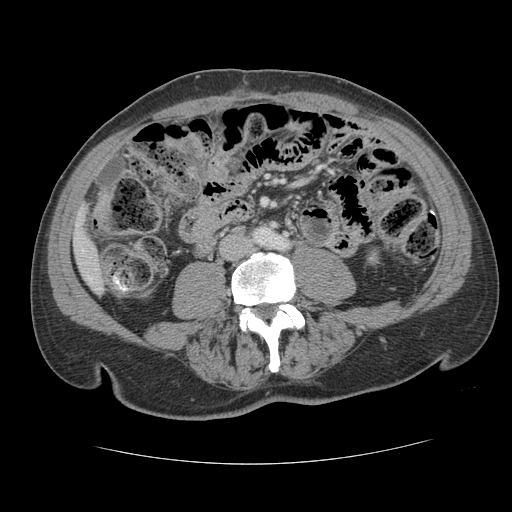
Contrast-enhanced abdominal CT, one axial slice. Slice 21 of 134 in the series (ordered by position). Intravenous contrast given. Soft-tissue window (W 400 / L 40 HU). 2.5 mm slice thickness. 512 × 512 image matrix. Male patient, age 68 years. Case-level facts recorded for this patient, not image findings: diagnosis: colorectal cancer liver metastases, imaged before liver resection; multiple liver metastases: yes; largest metastasis: 2.2 cm; chemotherapy before resection: no.
Outlined on this slice (manually delineated by an expert):
- liver: bounding box [x1, y1, x2, y2] px = [75, 229, 102, 290]
- planned liver remnant (the part of the liver to remain after resection): [75, 223, 102, 290]